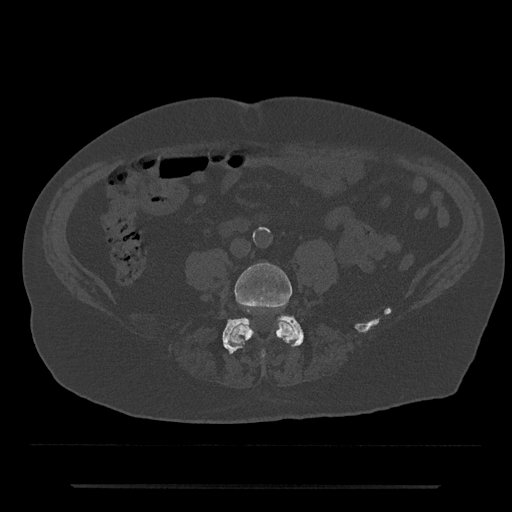
CT including the spine, one axial slice. Slice 326 of 797 in the series (ordered by position). 120 kVp. Bone window (W 1800 / L 400 HU). 0.5 mm slice thickness. 512 × 512 image matrix, field of view 434 × 434 mm. Male patient, age 80 years. From the clinical record (not read from this slice): primary cancer: prostate; vertebrae with lytic lesions (as recorded): L1, T11.
Structures marked on this image (semi-automatic segmentation, software-assisted and operator-edited):
- L4 vertebra: bounding box (x1, y1, x2, y2) in pixels: (228, 263, 297, 357)
- L5 vertebra: (222, 316, 304, 354)